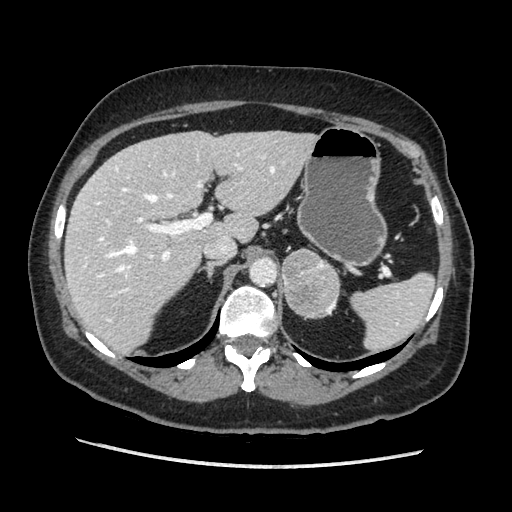
Contrast-enhanced abdominal CT, one axial slice. Slice 132 of 203 in the series (ordered by position). Soft-tissue window (W 400 / L 40 HU). 1.25 mm slice thickness. 512 × 512 image matrix, field of view 360 × 360 mm. Female patient. Case-level facts recorded for this patient, not image findings: diagnosis: adrenocortical carcinoma; tumour side: left adrenal; tumour size at pathology: 6.5 cm; Ki-67 index: 22 %; stage (as recorded): 2.
Structures marked on this image (semi-automatic segmentation, software-assisted and operator-edited):
- mass: bounding box (x1, y1, x2, y2) in pixels: (282, 249, 339, 318)